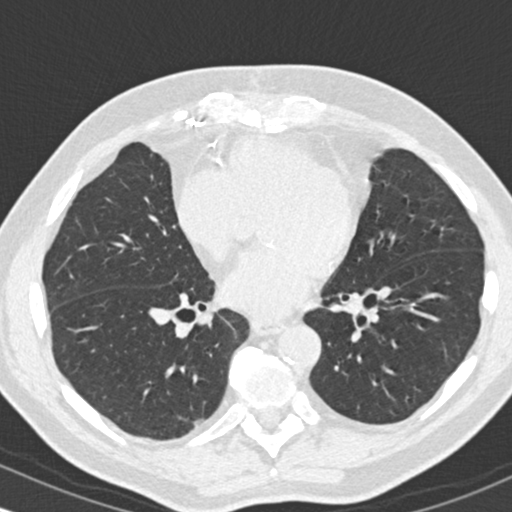
Chest CT (low-dose screening protocol), one axial image. Second annual screen. Lung window (W 1500 / L -600 HU). Standard (soft-tissue) reconstruction kernel (B30f). Slice 103 of 180 in the series. 512 × 512 image matrix, field of view 318 × 318 mm. Male participant, aged 68 years at enrolment. Former smoker at enrolment.
Lesion marked by an expert reader, box from (x=166, y=399) to (x=215, y=447) px. The screening reader recorded 2 non-calcified nodules or masses ≥4 mm on this exam (lingula, right upper lobe); which of them this box marks is not recorded. Official screen result: positive, no significant change: stable abnormalities potentially related to lung cancer, unchanged since the prior screening exam.